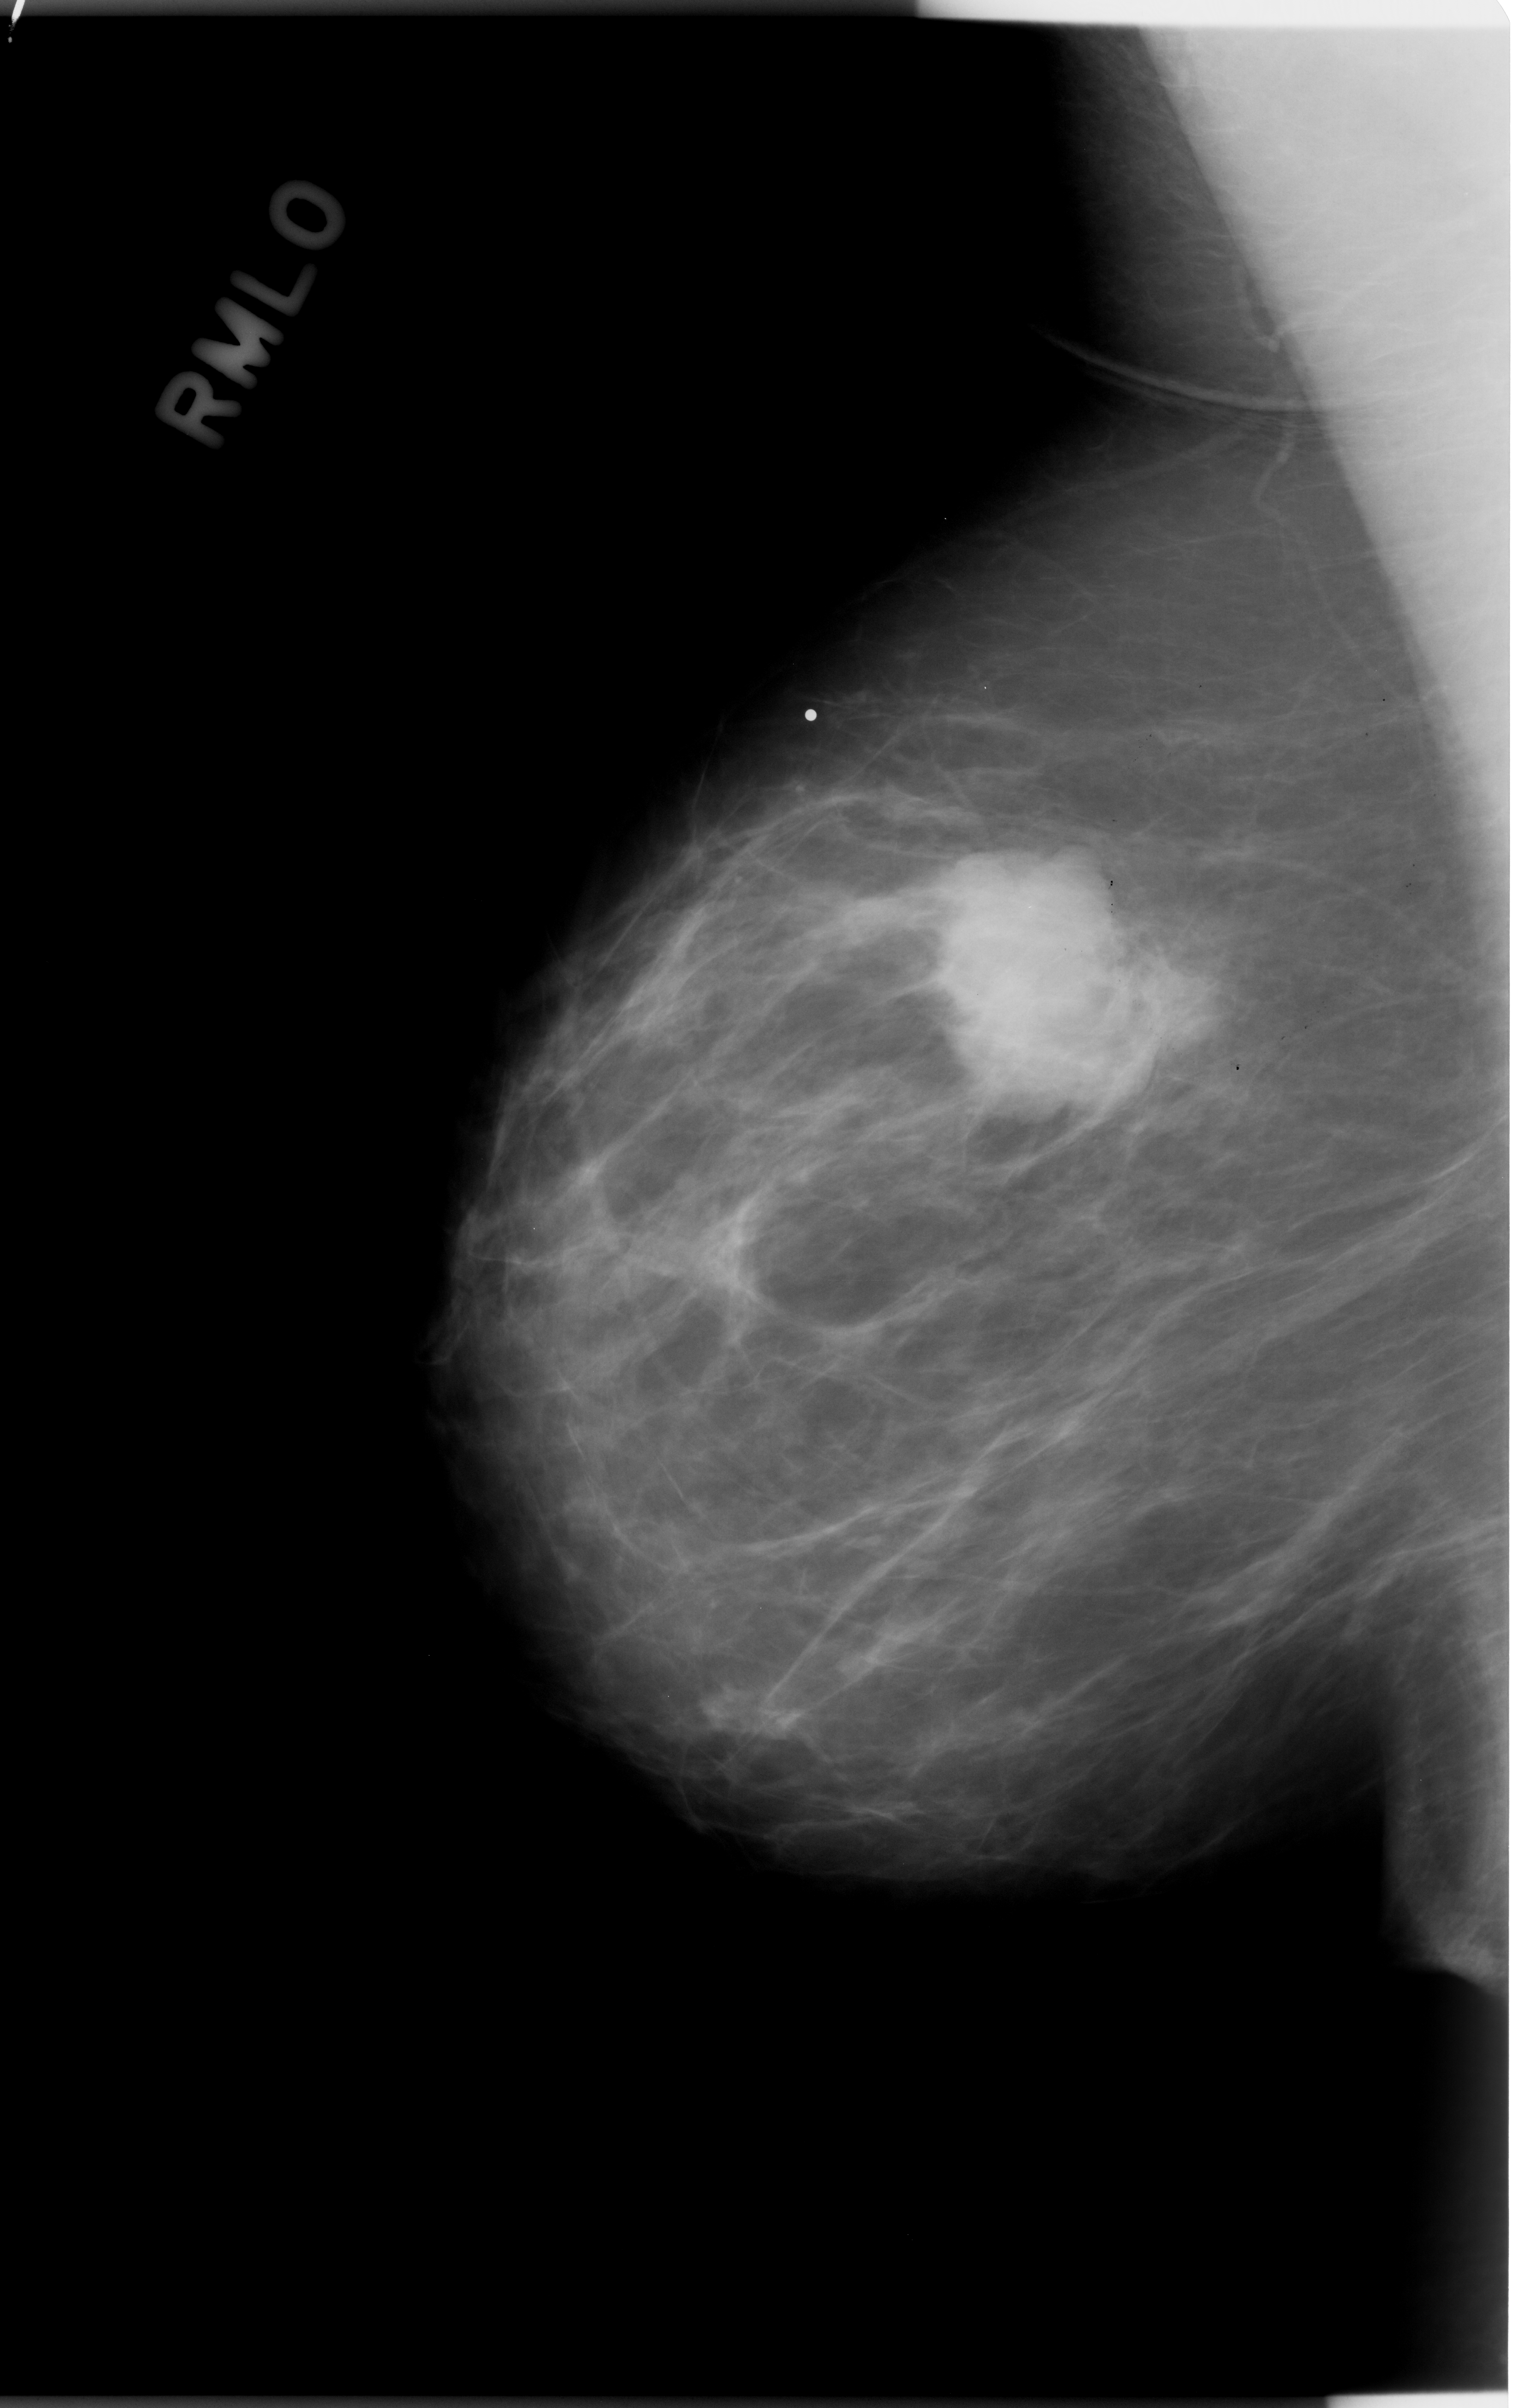
Mammogram (digitized film); right breast; mediolateral oblique (MLO) view; 1513 × 2408 image matrix.
Marked abnormalities (boxes around the expert regions of interest):
- mass, shape lobulated, margins microlobulated; BI-RADS assessment category 5; subtlety rating 5 on a 1 (subtle) to 5 (obvious) scale; pathology result (as recorded, not read from the image): malignant: box from (x=882, y=843) to (x=1155, y=1111) px